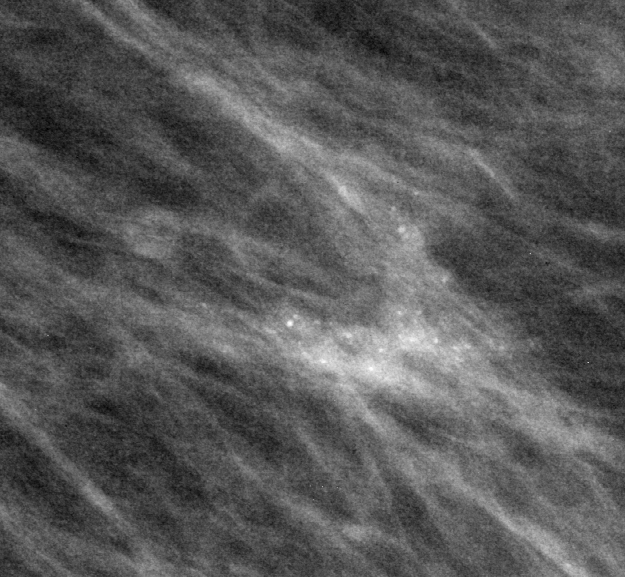
Cropped region of a digitized screen-film mammogram centred on a radiologist-marked abnormality; left breast; MLO view; BI-RADS breast density category 2 (scale 1–4).
Finding: calcifications, morphology pleomorphic, distribution clustered; BI-RADS assessment category 4; pathology (as recorded): malignant.